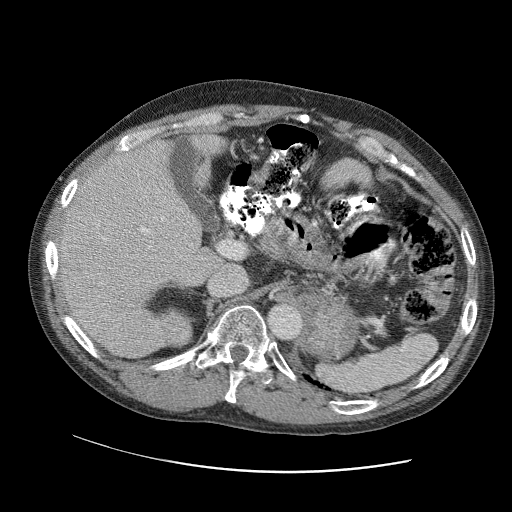
Contrast-enhanced abdominal CT (liver protocol), one axial slice. Position 67 of 109 along the scan axis. Soft-tissue window (W 400 / L 40 HU). 2.5 mm slice thickness. 512 × 512 image matrix, field of view 400 × 400 mm. From the clinical record (not read from this slice): diagnosis: hepatocellular carcinoma (patient treated with transarterial chemoembolisation; whether this scan precedes or follows treatment is not stated here); TNM stage (as recorded): Stage-IIIC; Child-Pugh class: B; tumour nodularity: uninodular.
Outlined on this slice (semi-automatically segmented with operator editing):
- liver parenchyma outside the tumour (the mass and vessels are separate outlines, so this box may not span the whole liver): bounding box <54,136,225,358> (left, top, right, bottom; pixels)
- mass: <169,318,192,346>
- liver vessels: <85,148,165,314>